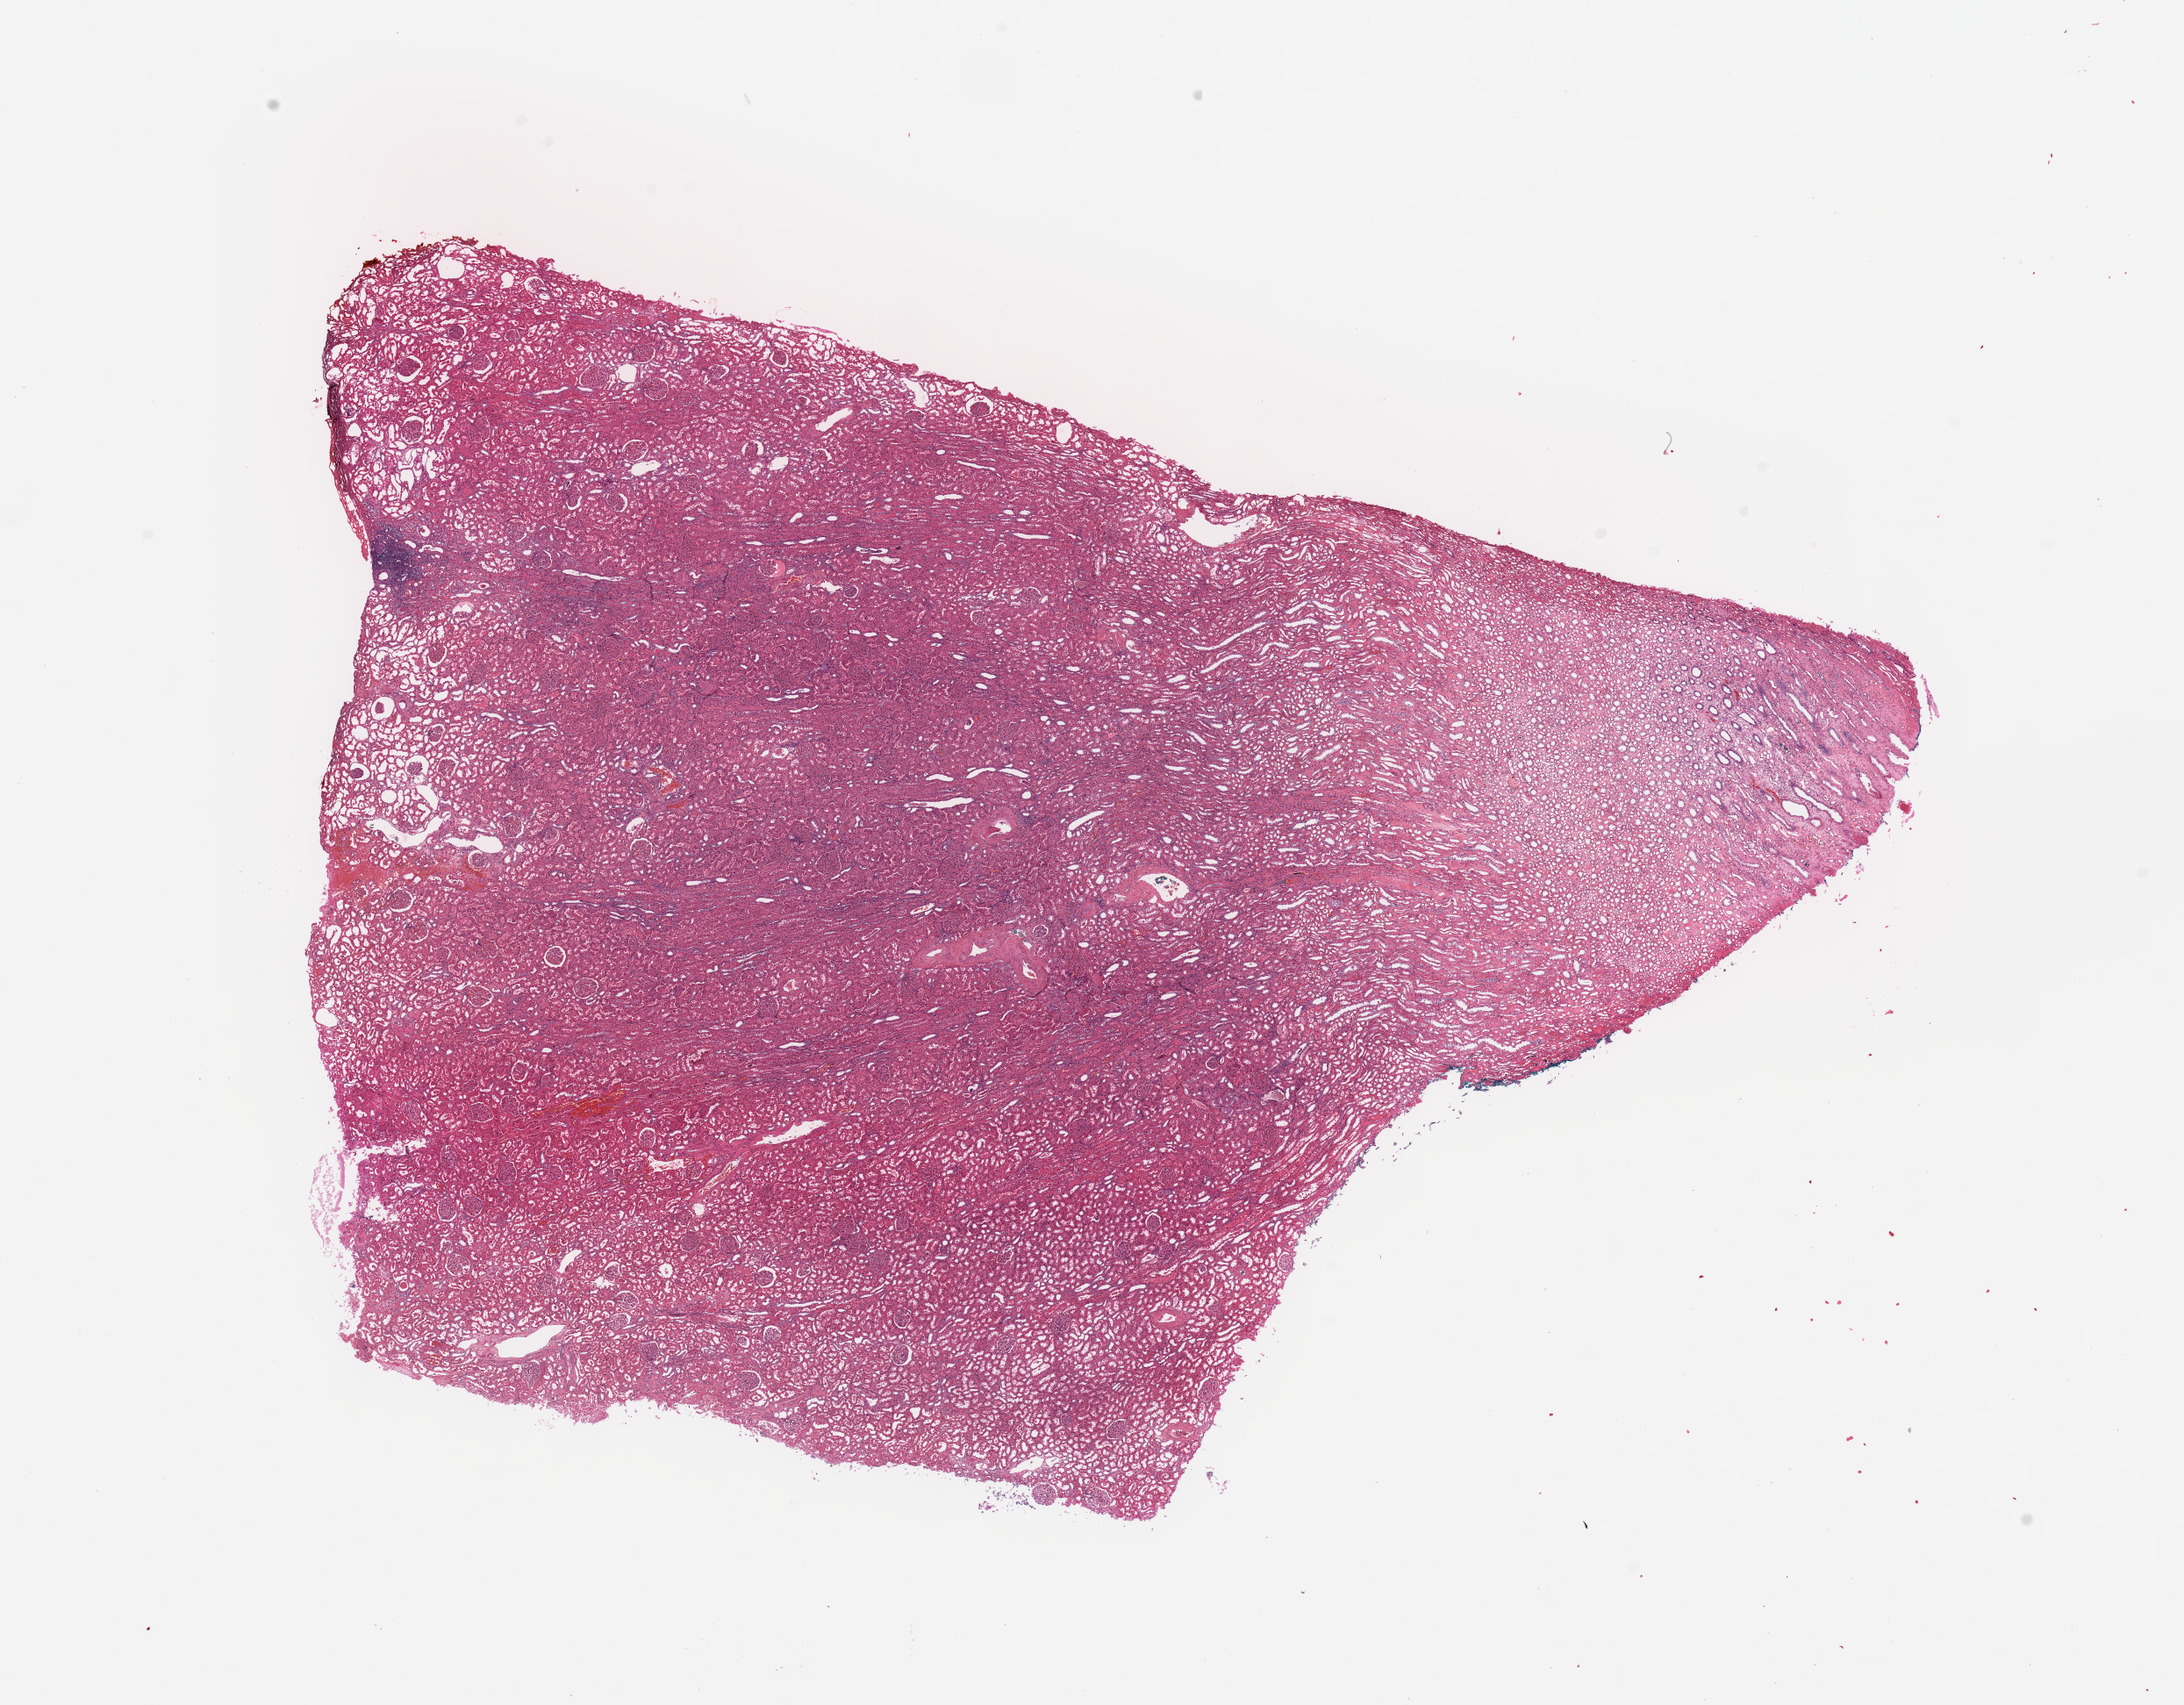
H&E-stained whole-slide image, low-resolution overview of the scanned area, about 19.7 x 15.4 mm; normal (non-tumour) tissue sample, sampled site: kidney. Patient: male, age 54 years.
This section: normal (non-tumour) tissue from the same patient. Patient diagnosis: Renal cell carcinoma, NOS.